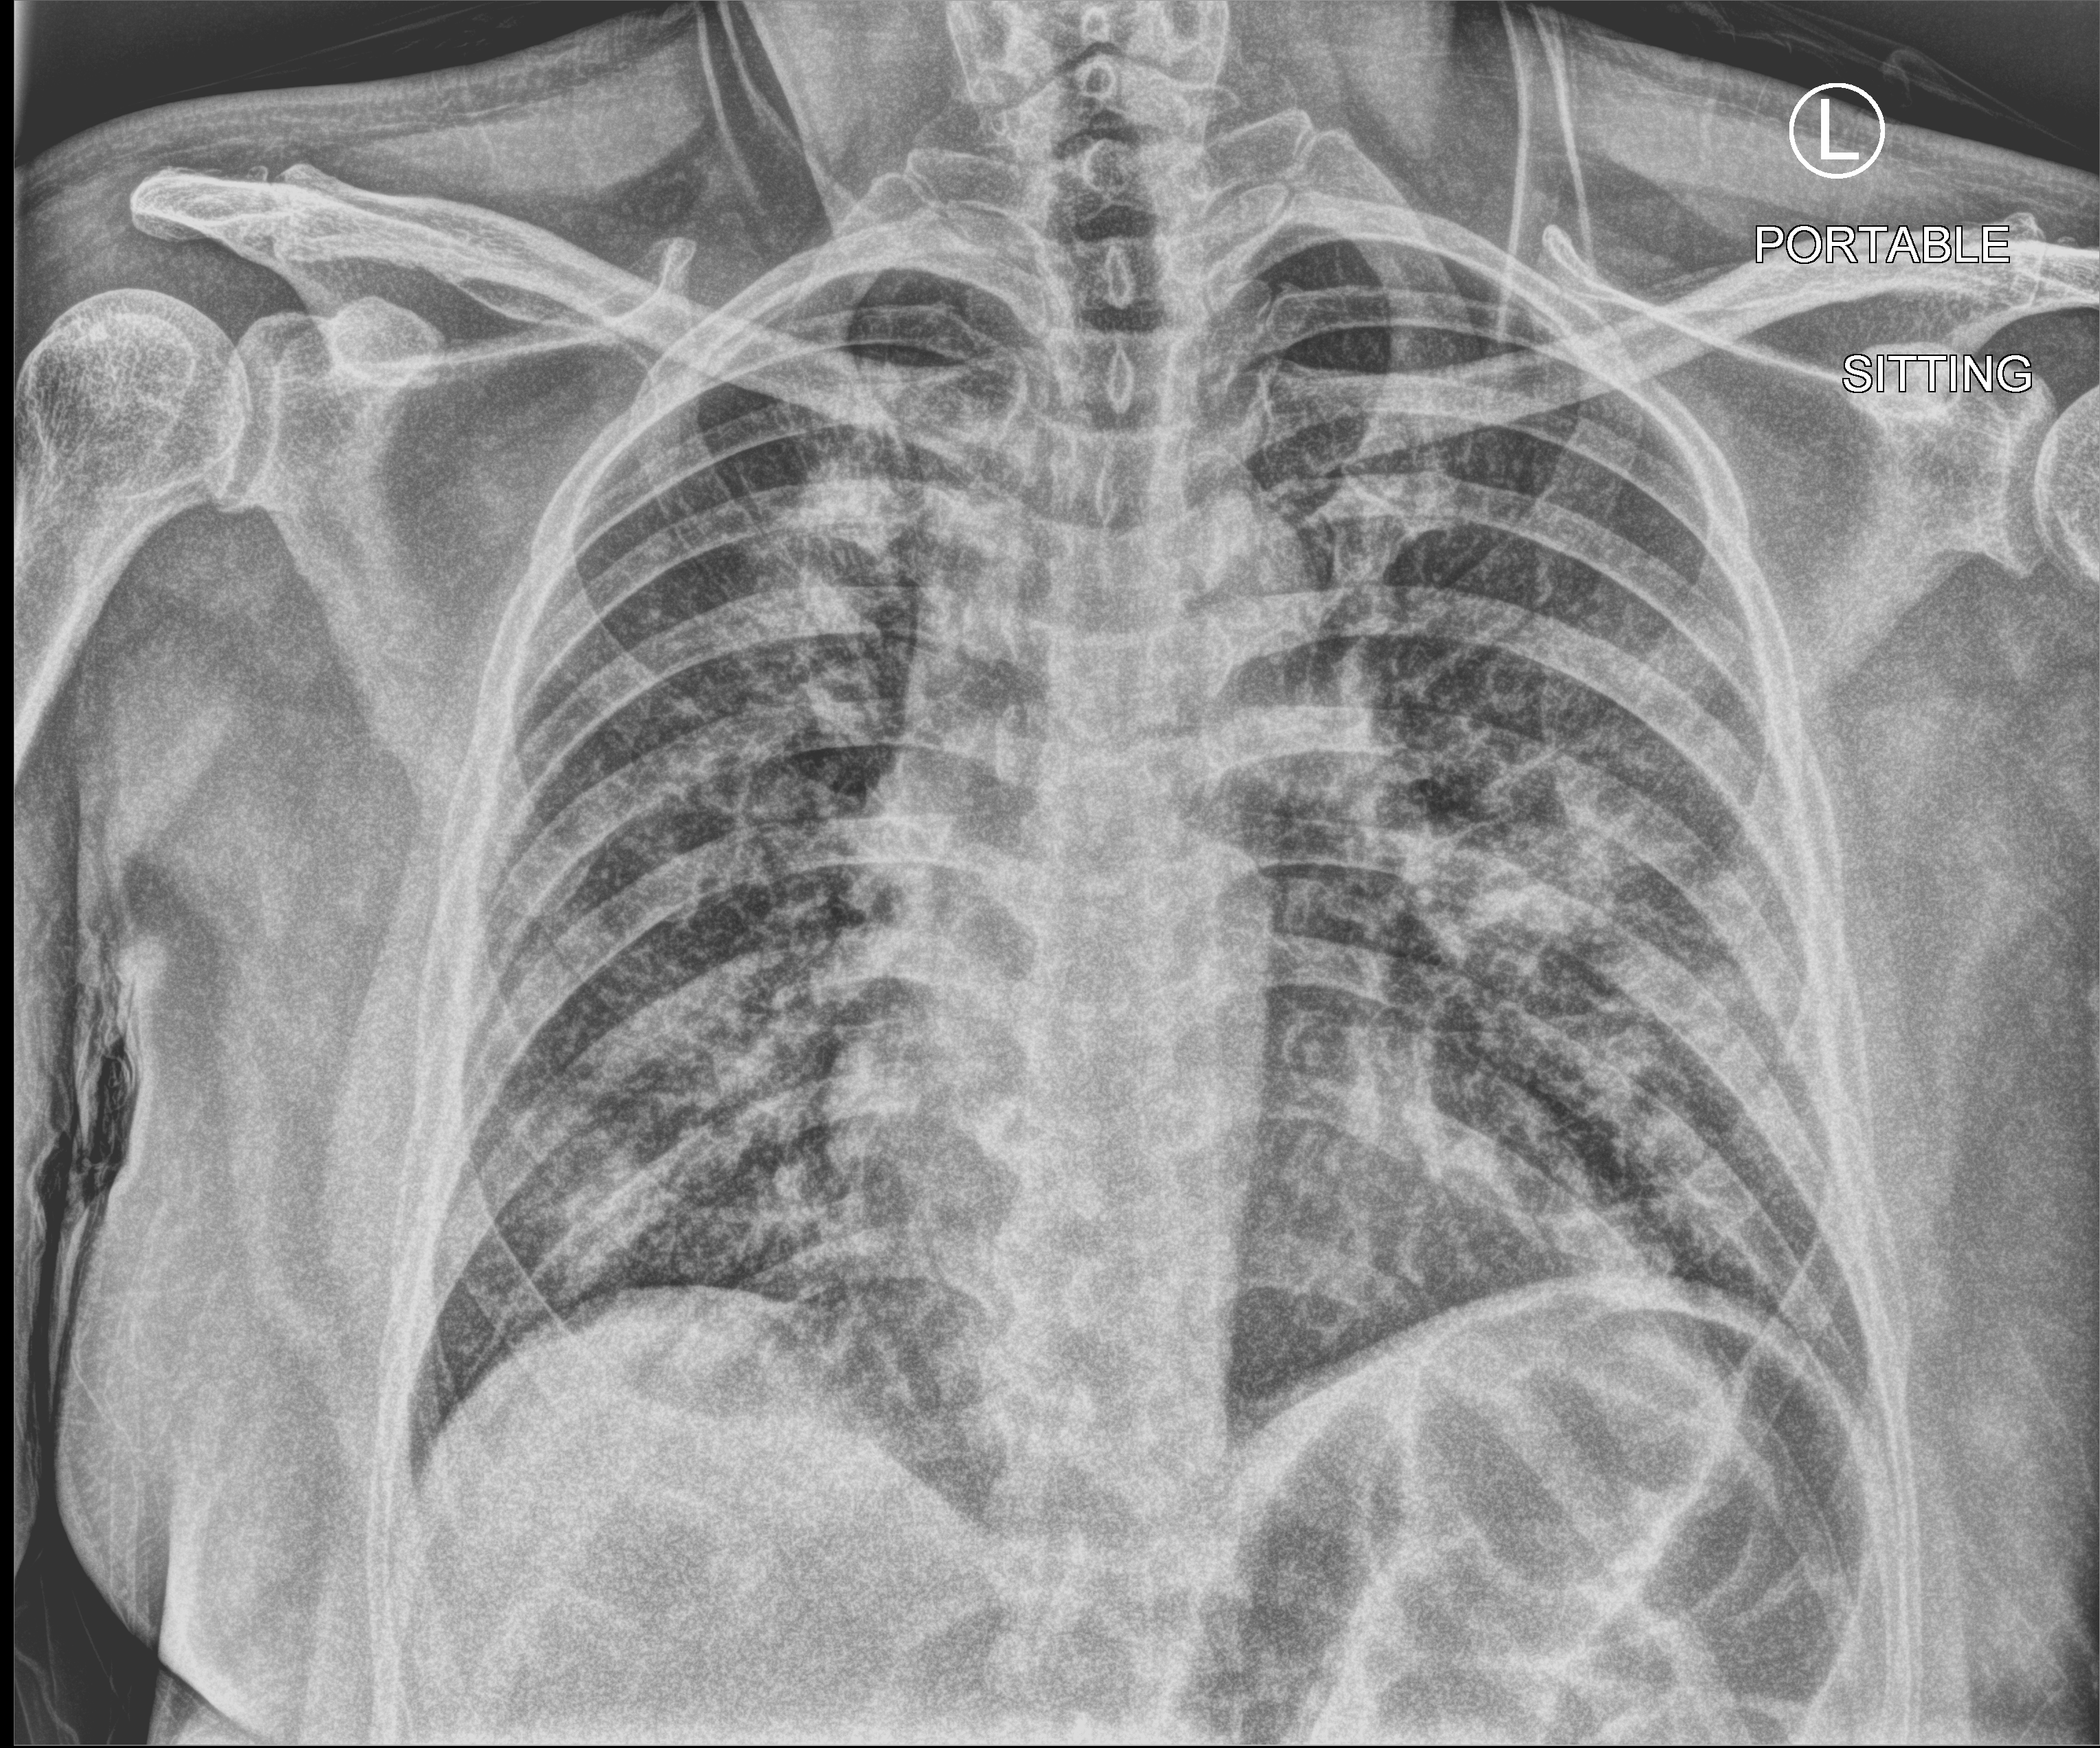
Portable chest radiograph. Male patient hospitalised with COVID-19, age 18–59 years.
From the hospital-stay record, not from the radiograph (when in the stay this image was taken is not recorded): mechanically ventilated during this hospital stay: no; smoking status (admission record): never; admitted to intensive care during this hospital stay: no.